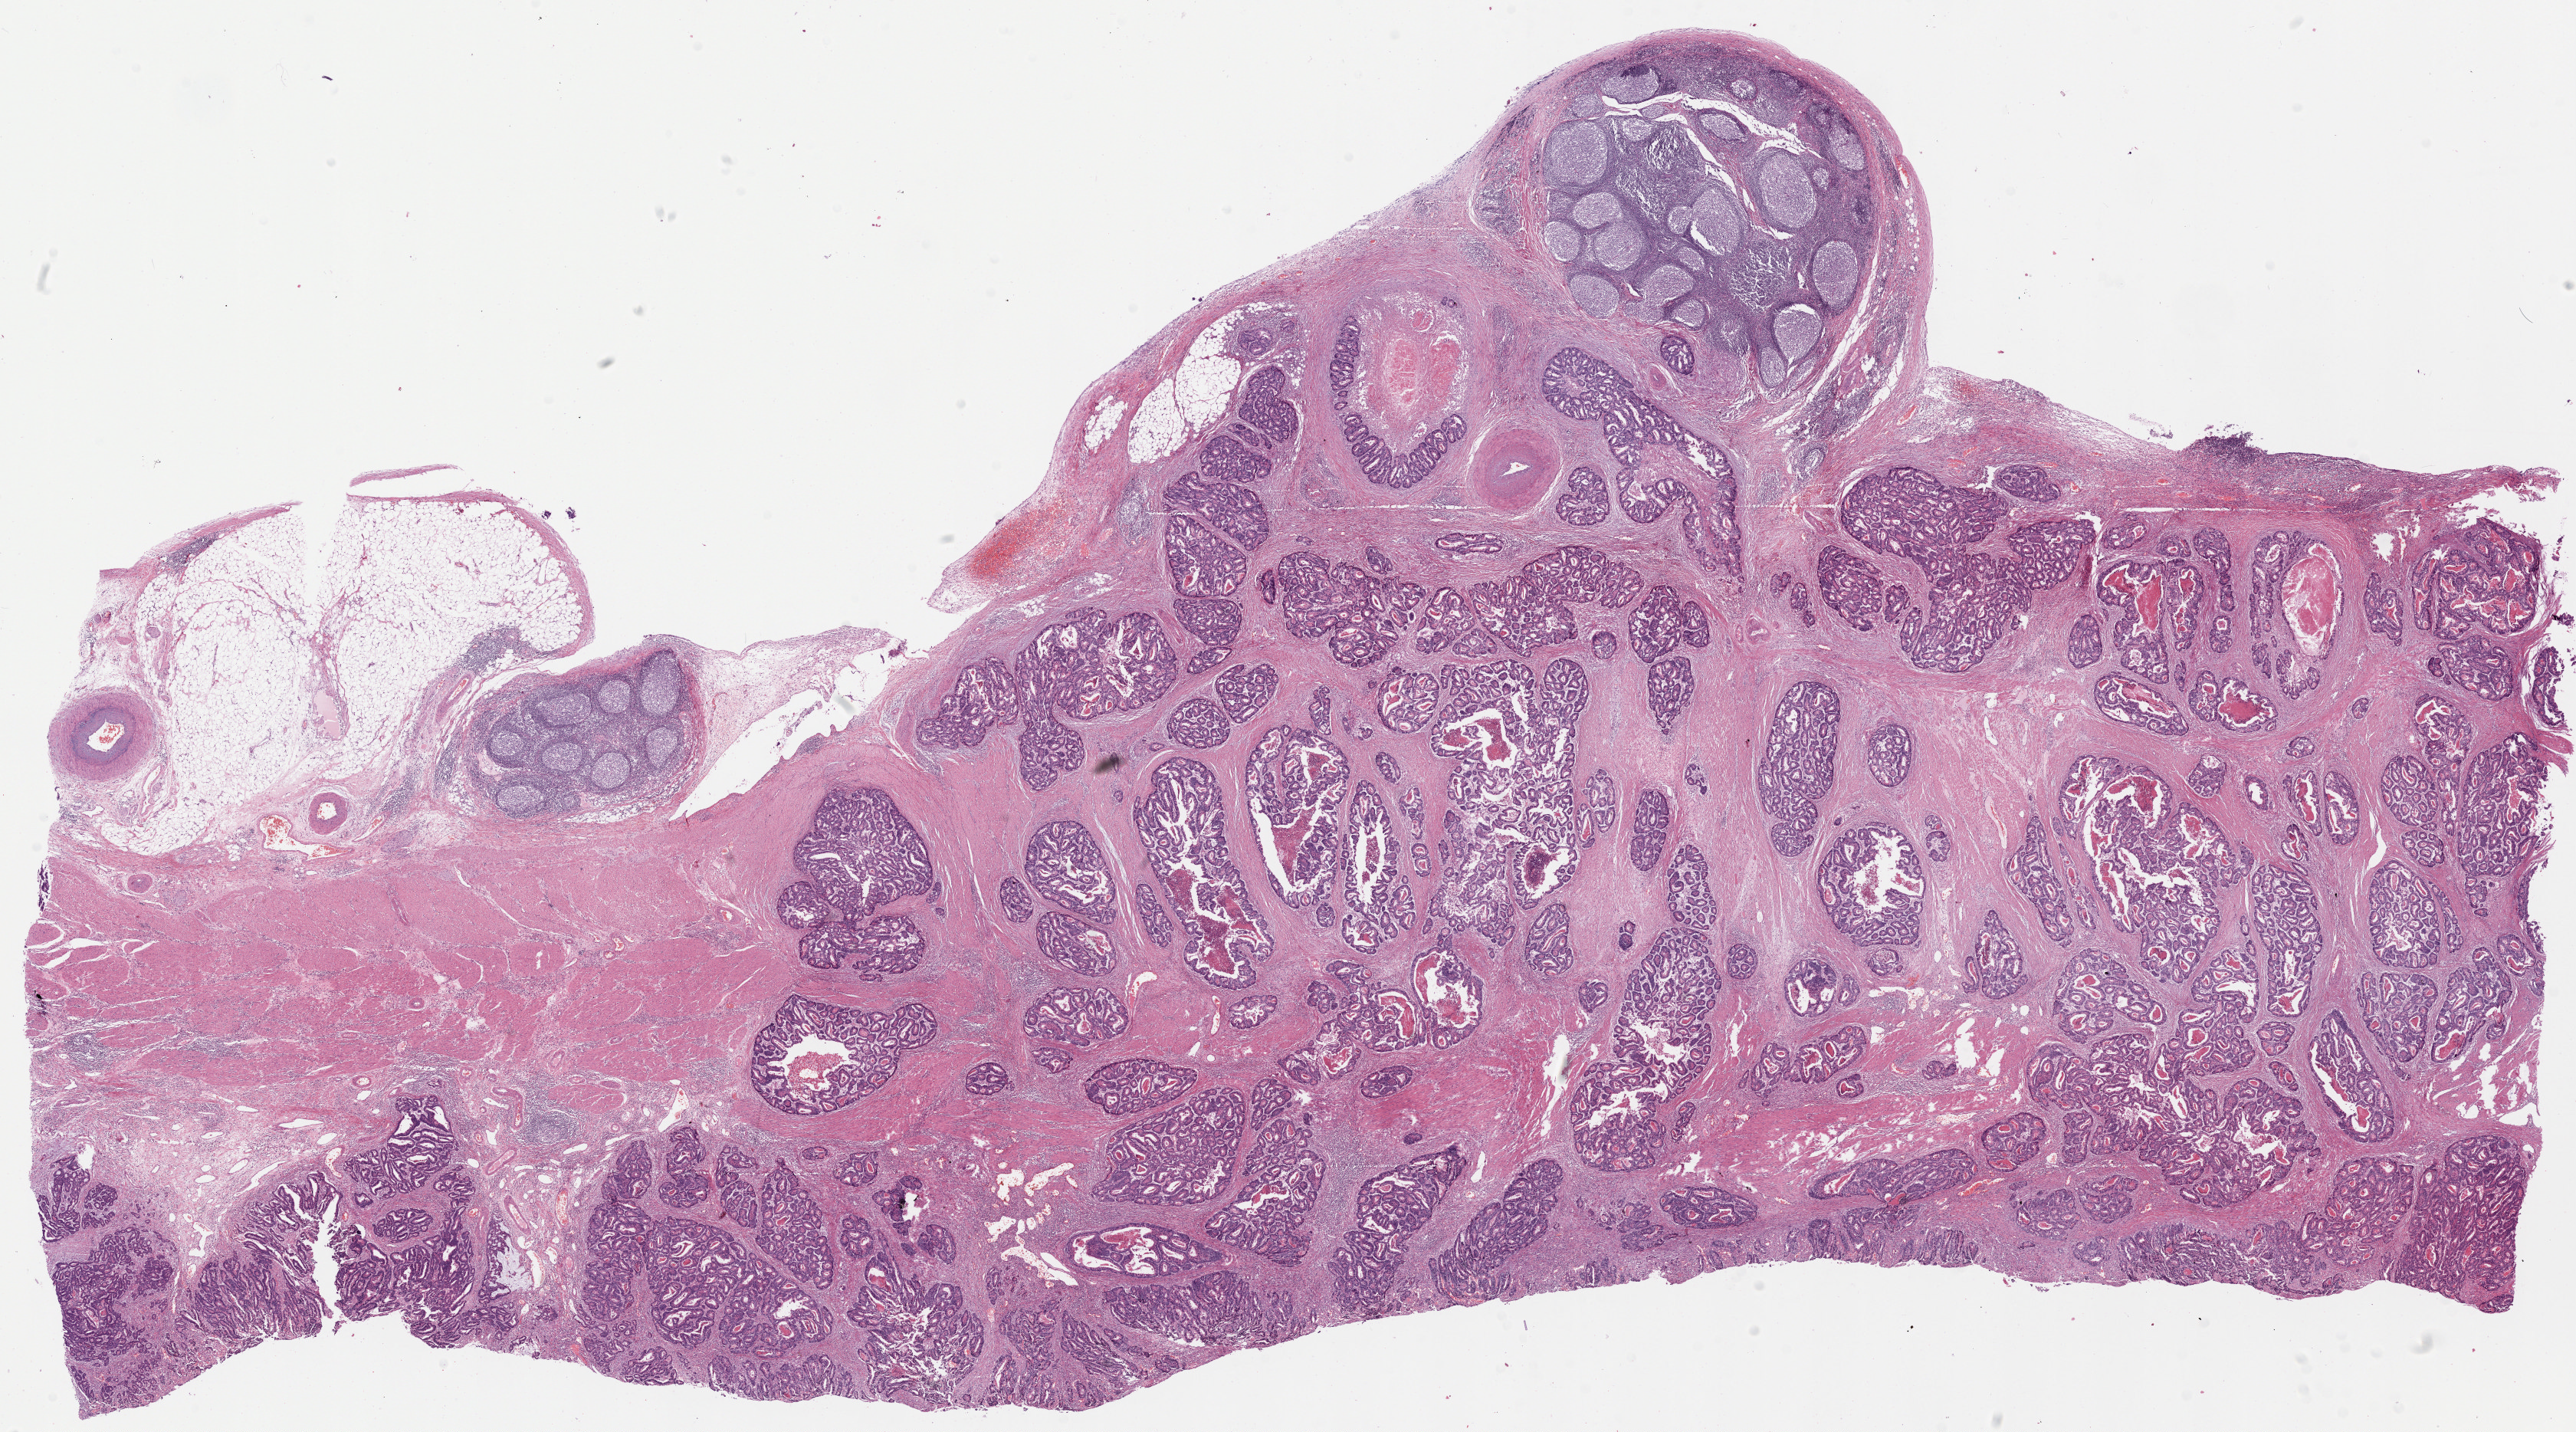
Digitized H&E-stained tissue section (whole slide) — low-resolution overview of the scanned area, about 26.6 x 14.8 mm (slide scanned at 20x). FFPE section. Sample: primary tumour, stomach. Male, age 76 years at initial diagnosis. Histologic grade: G2 (moderately differentiated).
- lymph nodes positive (case pathology): 5 of 99 examined
- histologic diagnosis: Tubular adenocarcinoma
- AJCC pathologic stage: IIIA